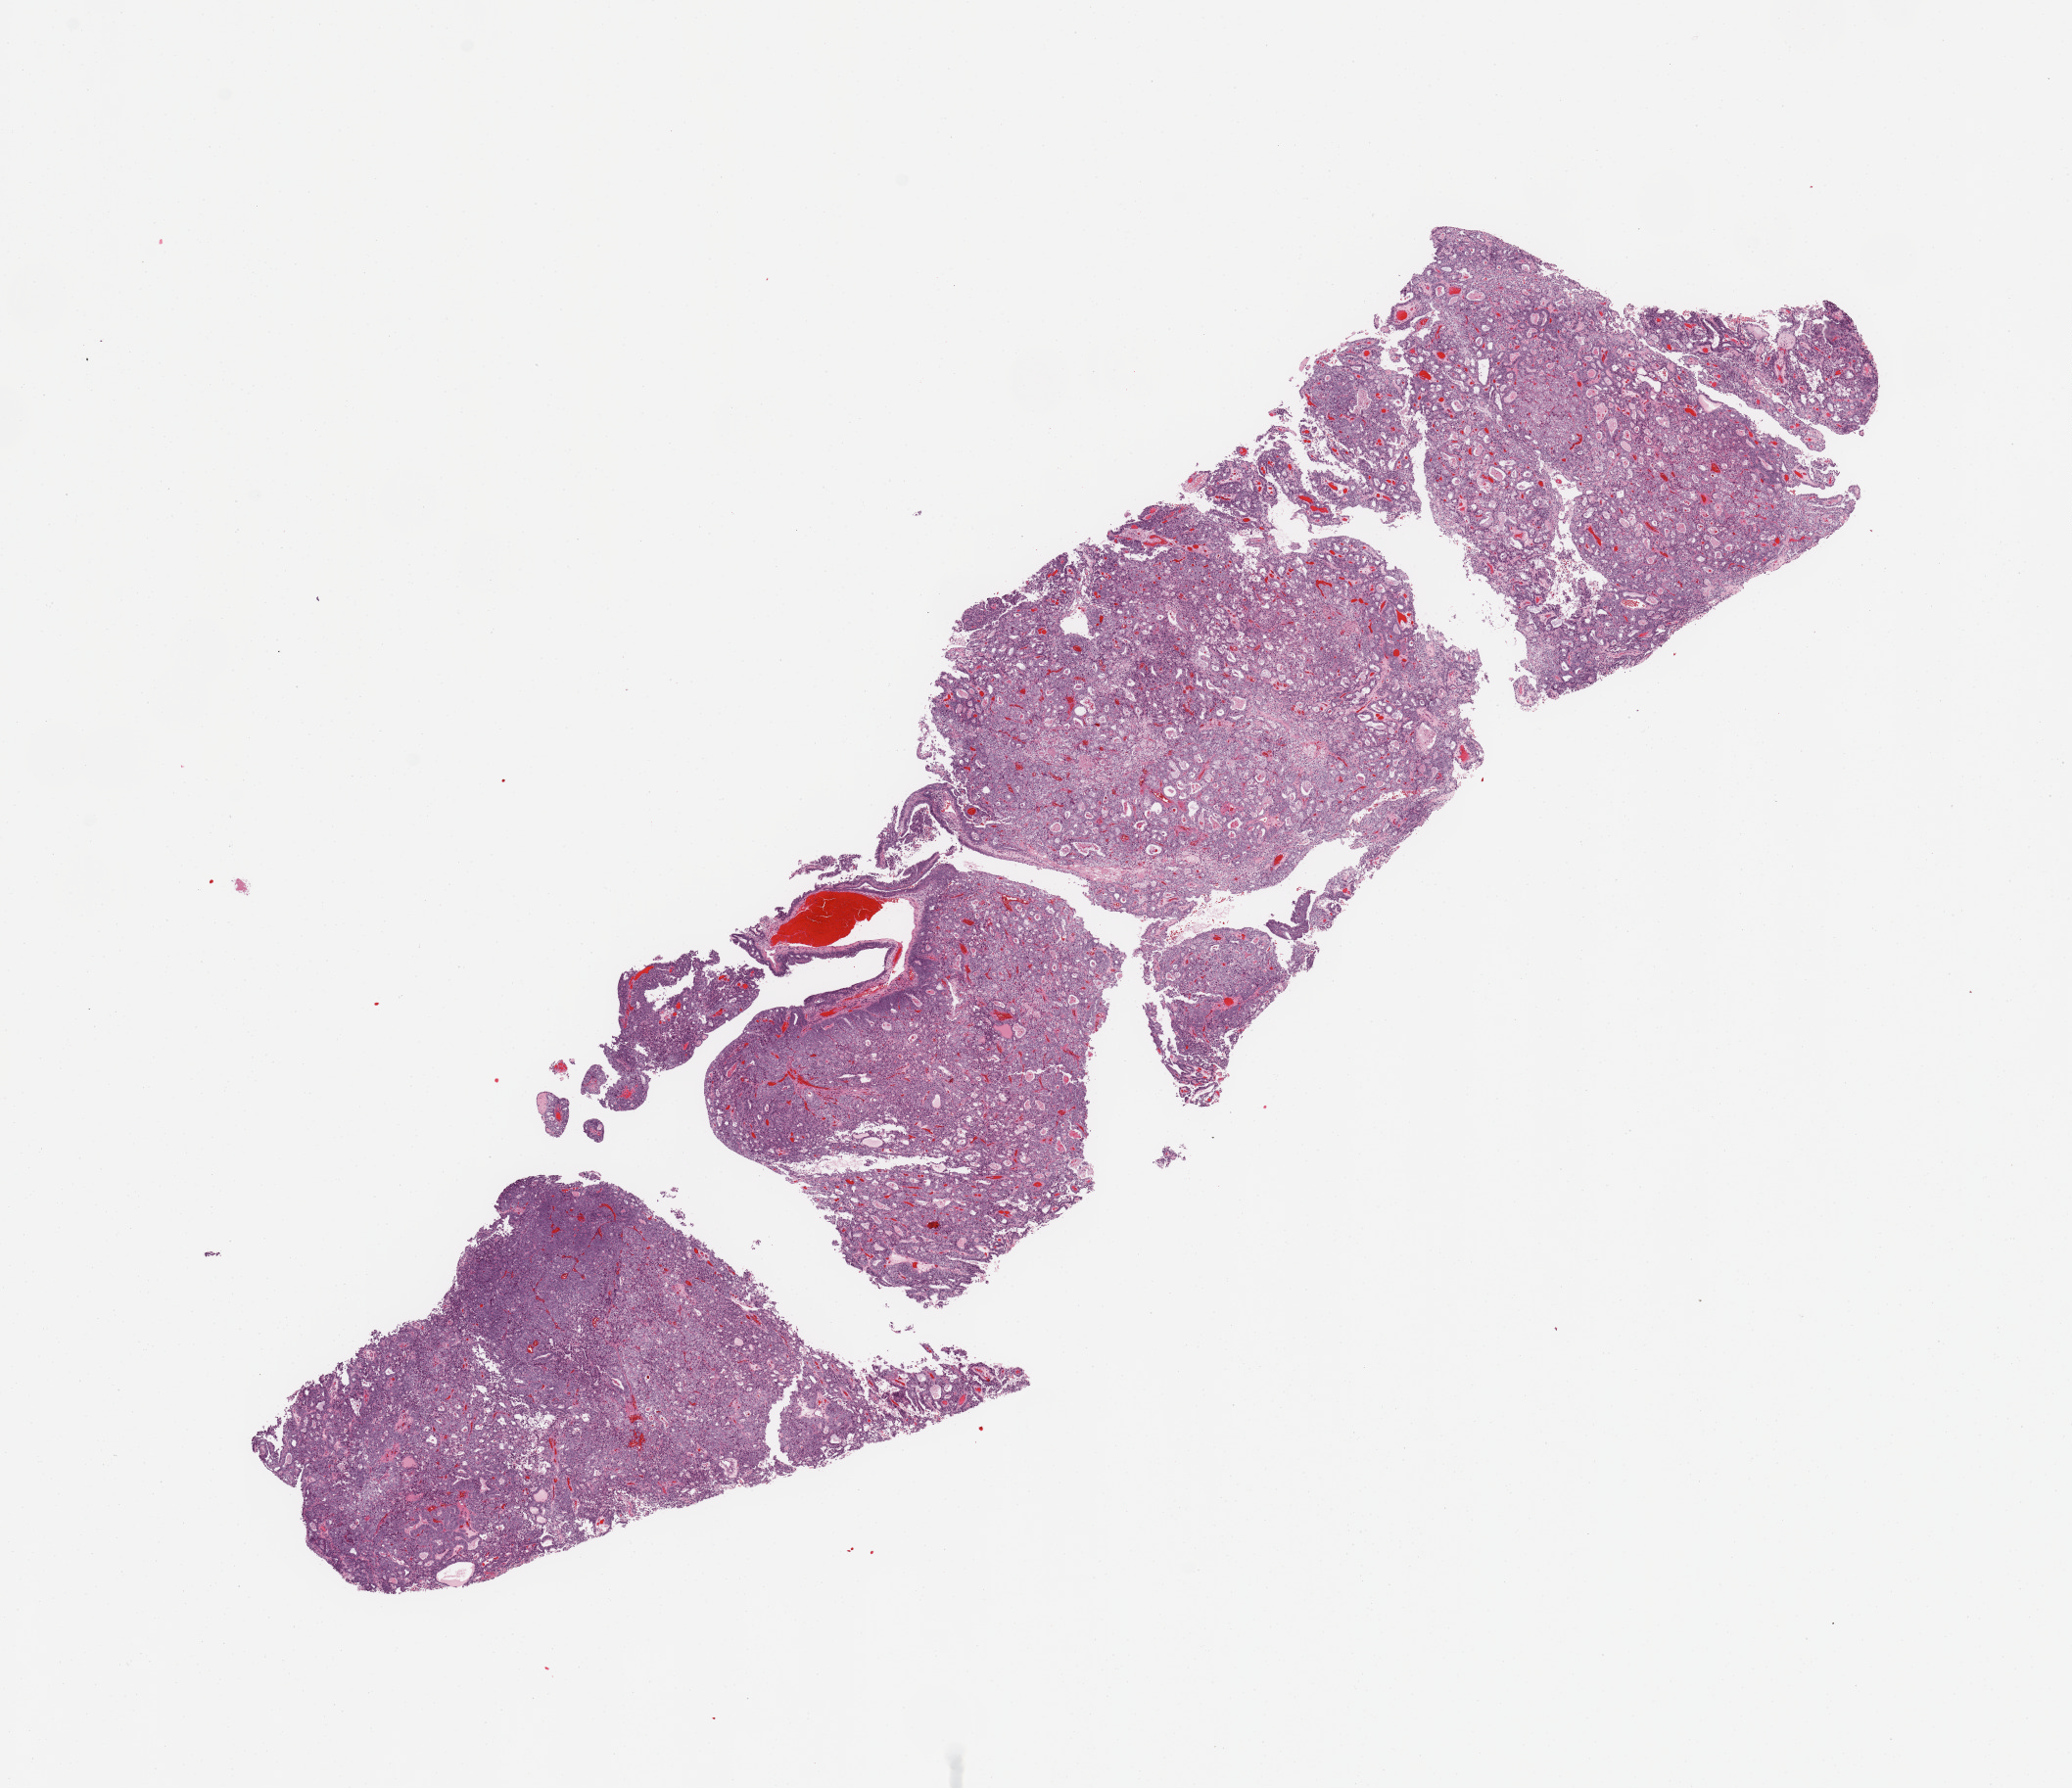
Whole-slide histology image, H&E, a low-resolution overview of the entire scanned area, about 16.7 x 14.4 mm (acquisition: 20x scan); uterus, tumour tissue. Patient: female, age 57 years. Histologic grade: G3 (poorly differentiated).
- diagnosis: Endometrioid adenocarcinoma, NOS
- AJCC pathologic stage: I